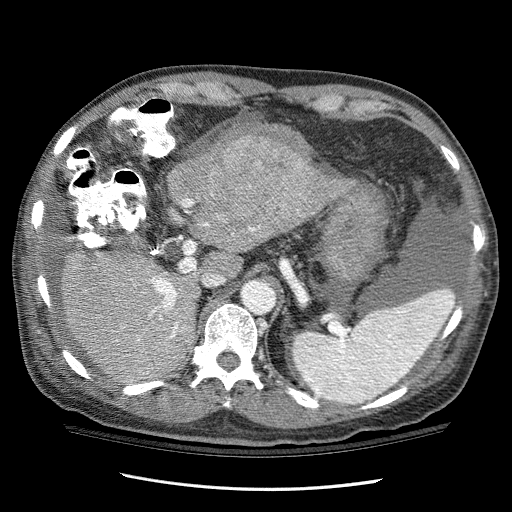
Contrast-enhanced abdominal CT (liver protocol), one axial slice; position 73 of 114 along the scan axis; reconstruction kernel STANDARD; 120 kVp; one of 3 acquisitions stored at this slice position; soft-tissue window (W 400 / L 40 HU); 512 × 512 image matrix, field of view 360 × 360 mm. Case-level facts recorded for this patient, not image findings: diagnosis: hepatocellular carcinoma (patient treated with transarterial chemoembolisation; whether this scan precedes or follows treatment is not stated here); TNM stage (as recorded): Stage-I.
Structures marked on this image (semi-automatic segmentation, software-assisted and operator-edited):
- liver parenchyma outside the tumour (the mass and vessels are separate outlines, so this box may not span the whole liver): bounding box <62,151,356,384> (left, top, right, bottom; pixels)
- mass: <210,119,316,203>
- liver vessels: <130,194,260,338>